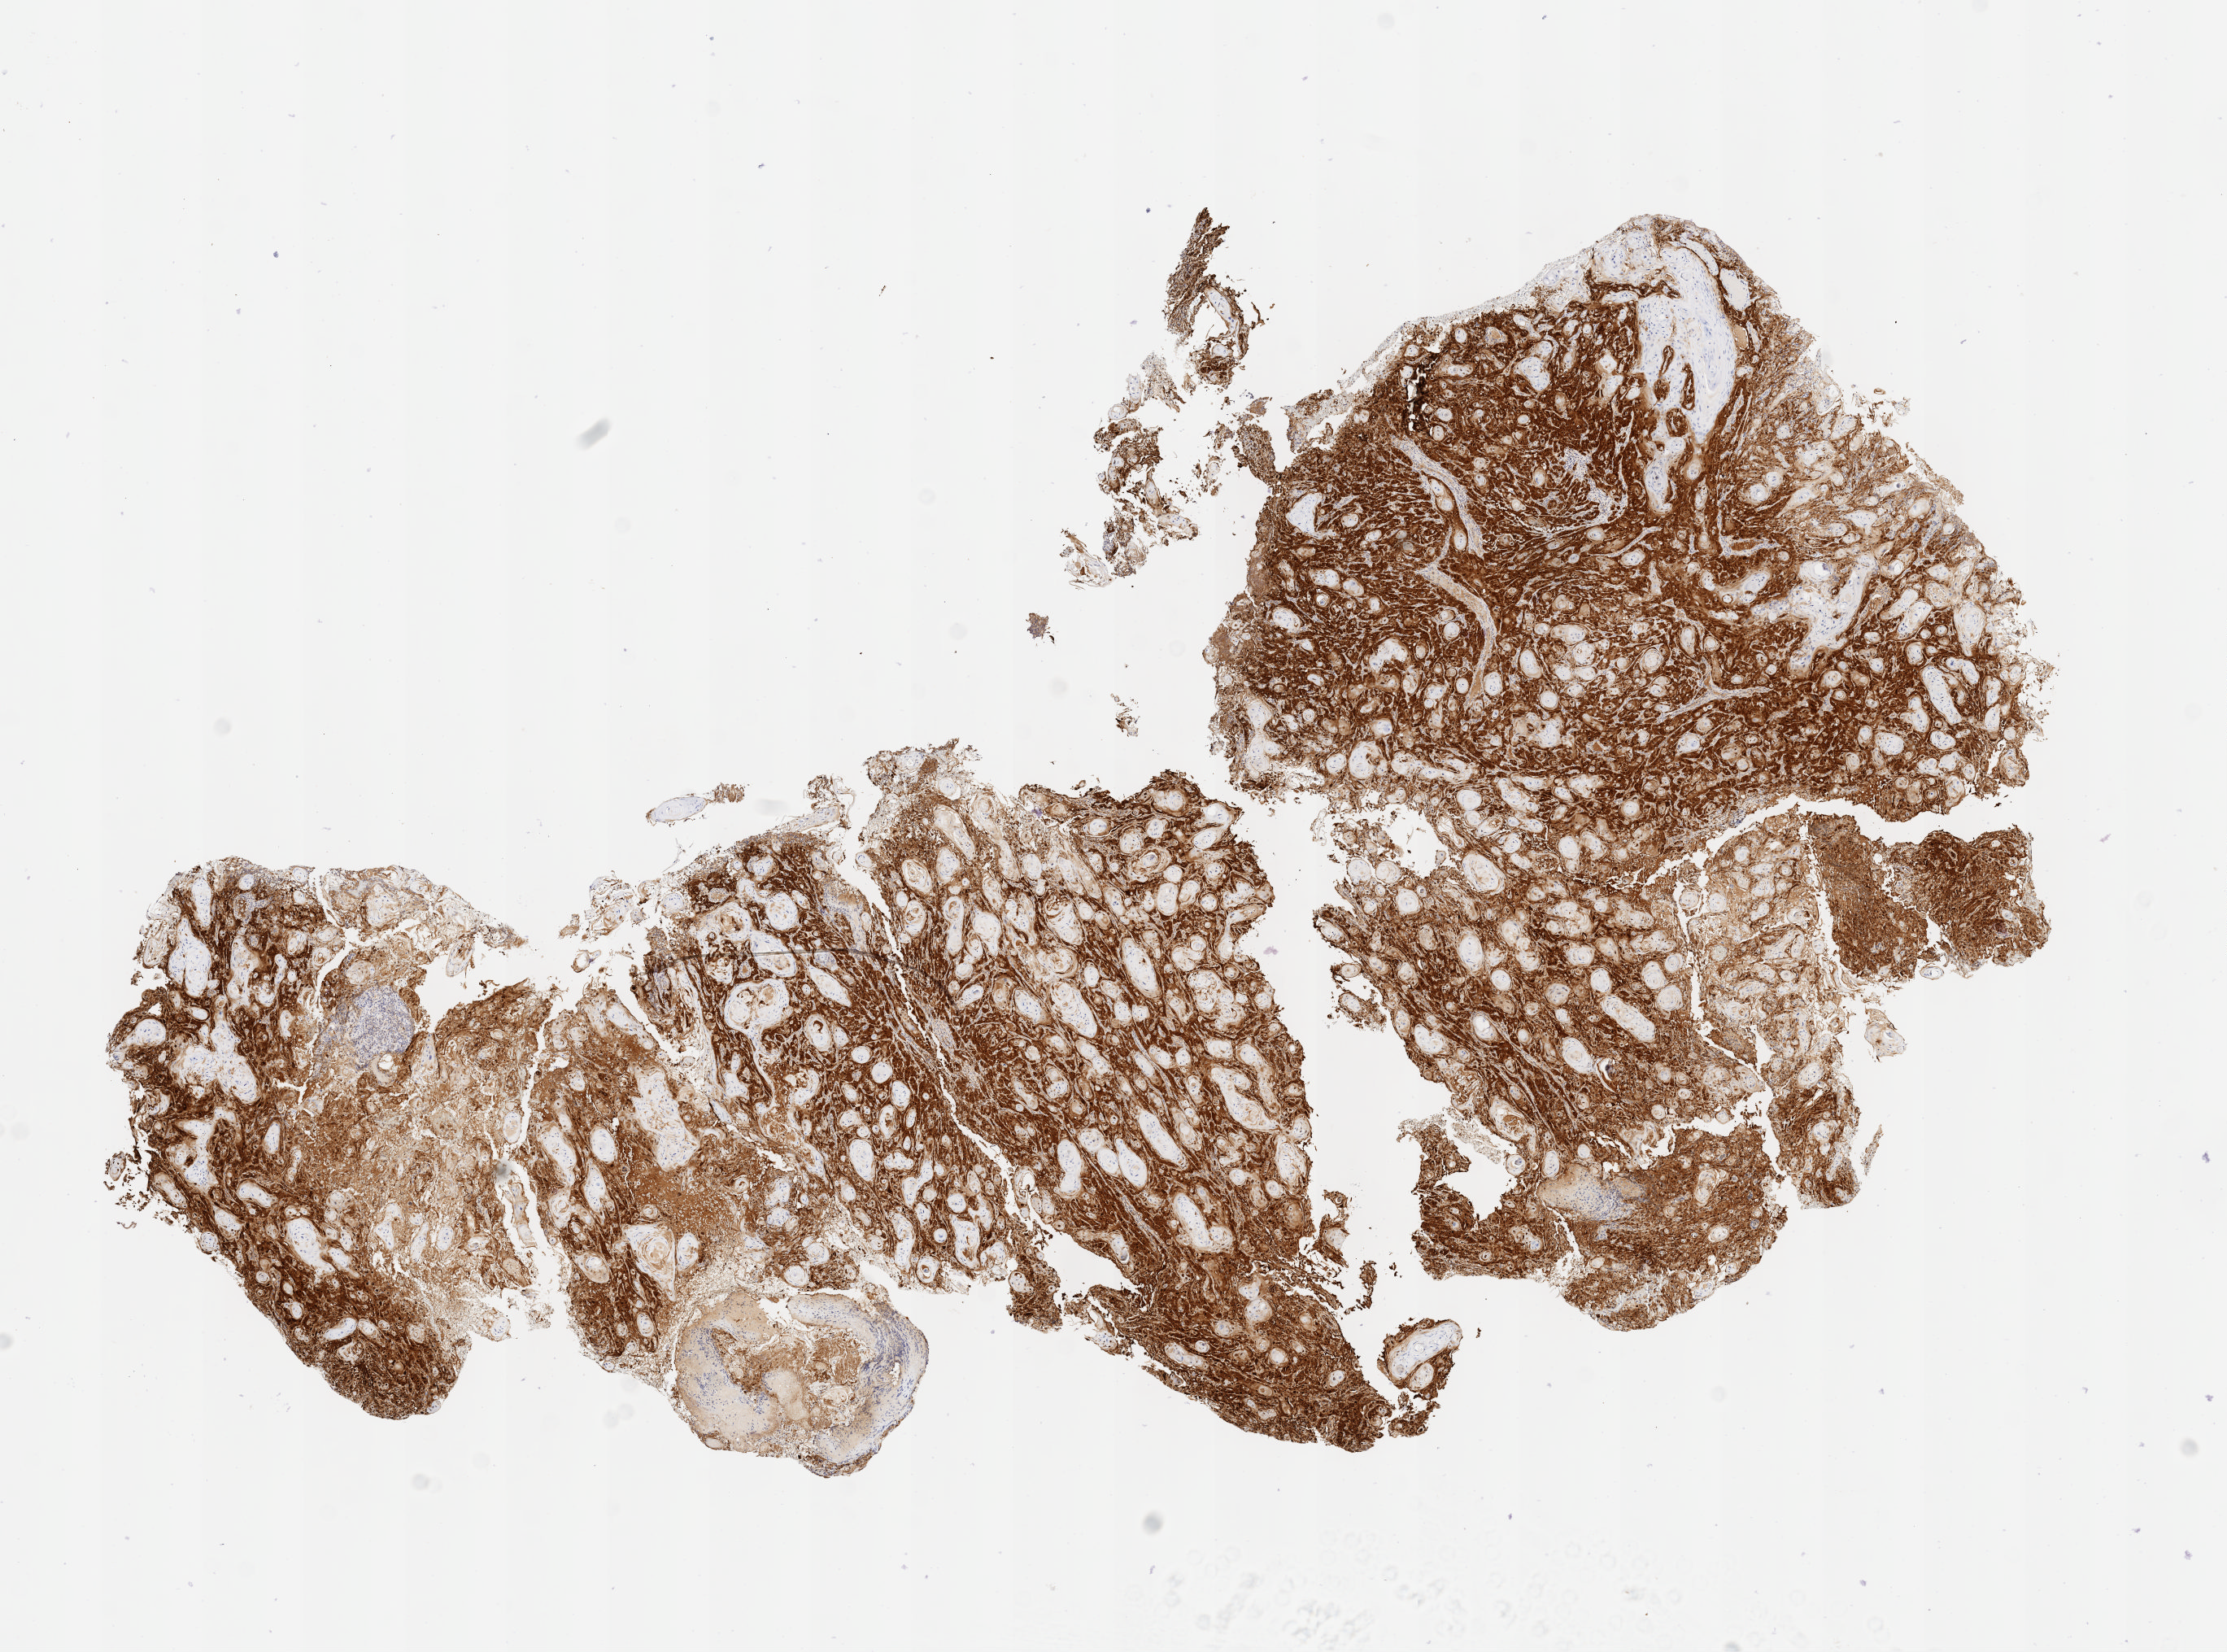
Whole-slide image, immunohistochemical stain for p16 (p16INK4a) — low-resolution overview of the scanned area, about 11.1 x 8.2 mm; tumor tissue; anatomic site: cervix. Patient female; aged 26.
Histologic diagnosis: Squamous cell carcinoma, keratinizing, NOS.